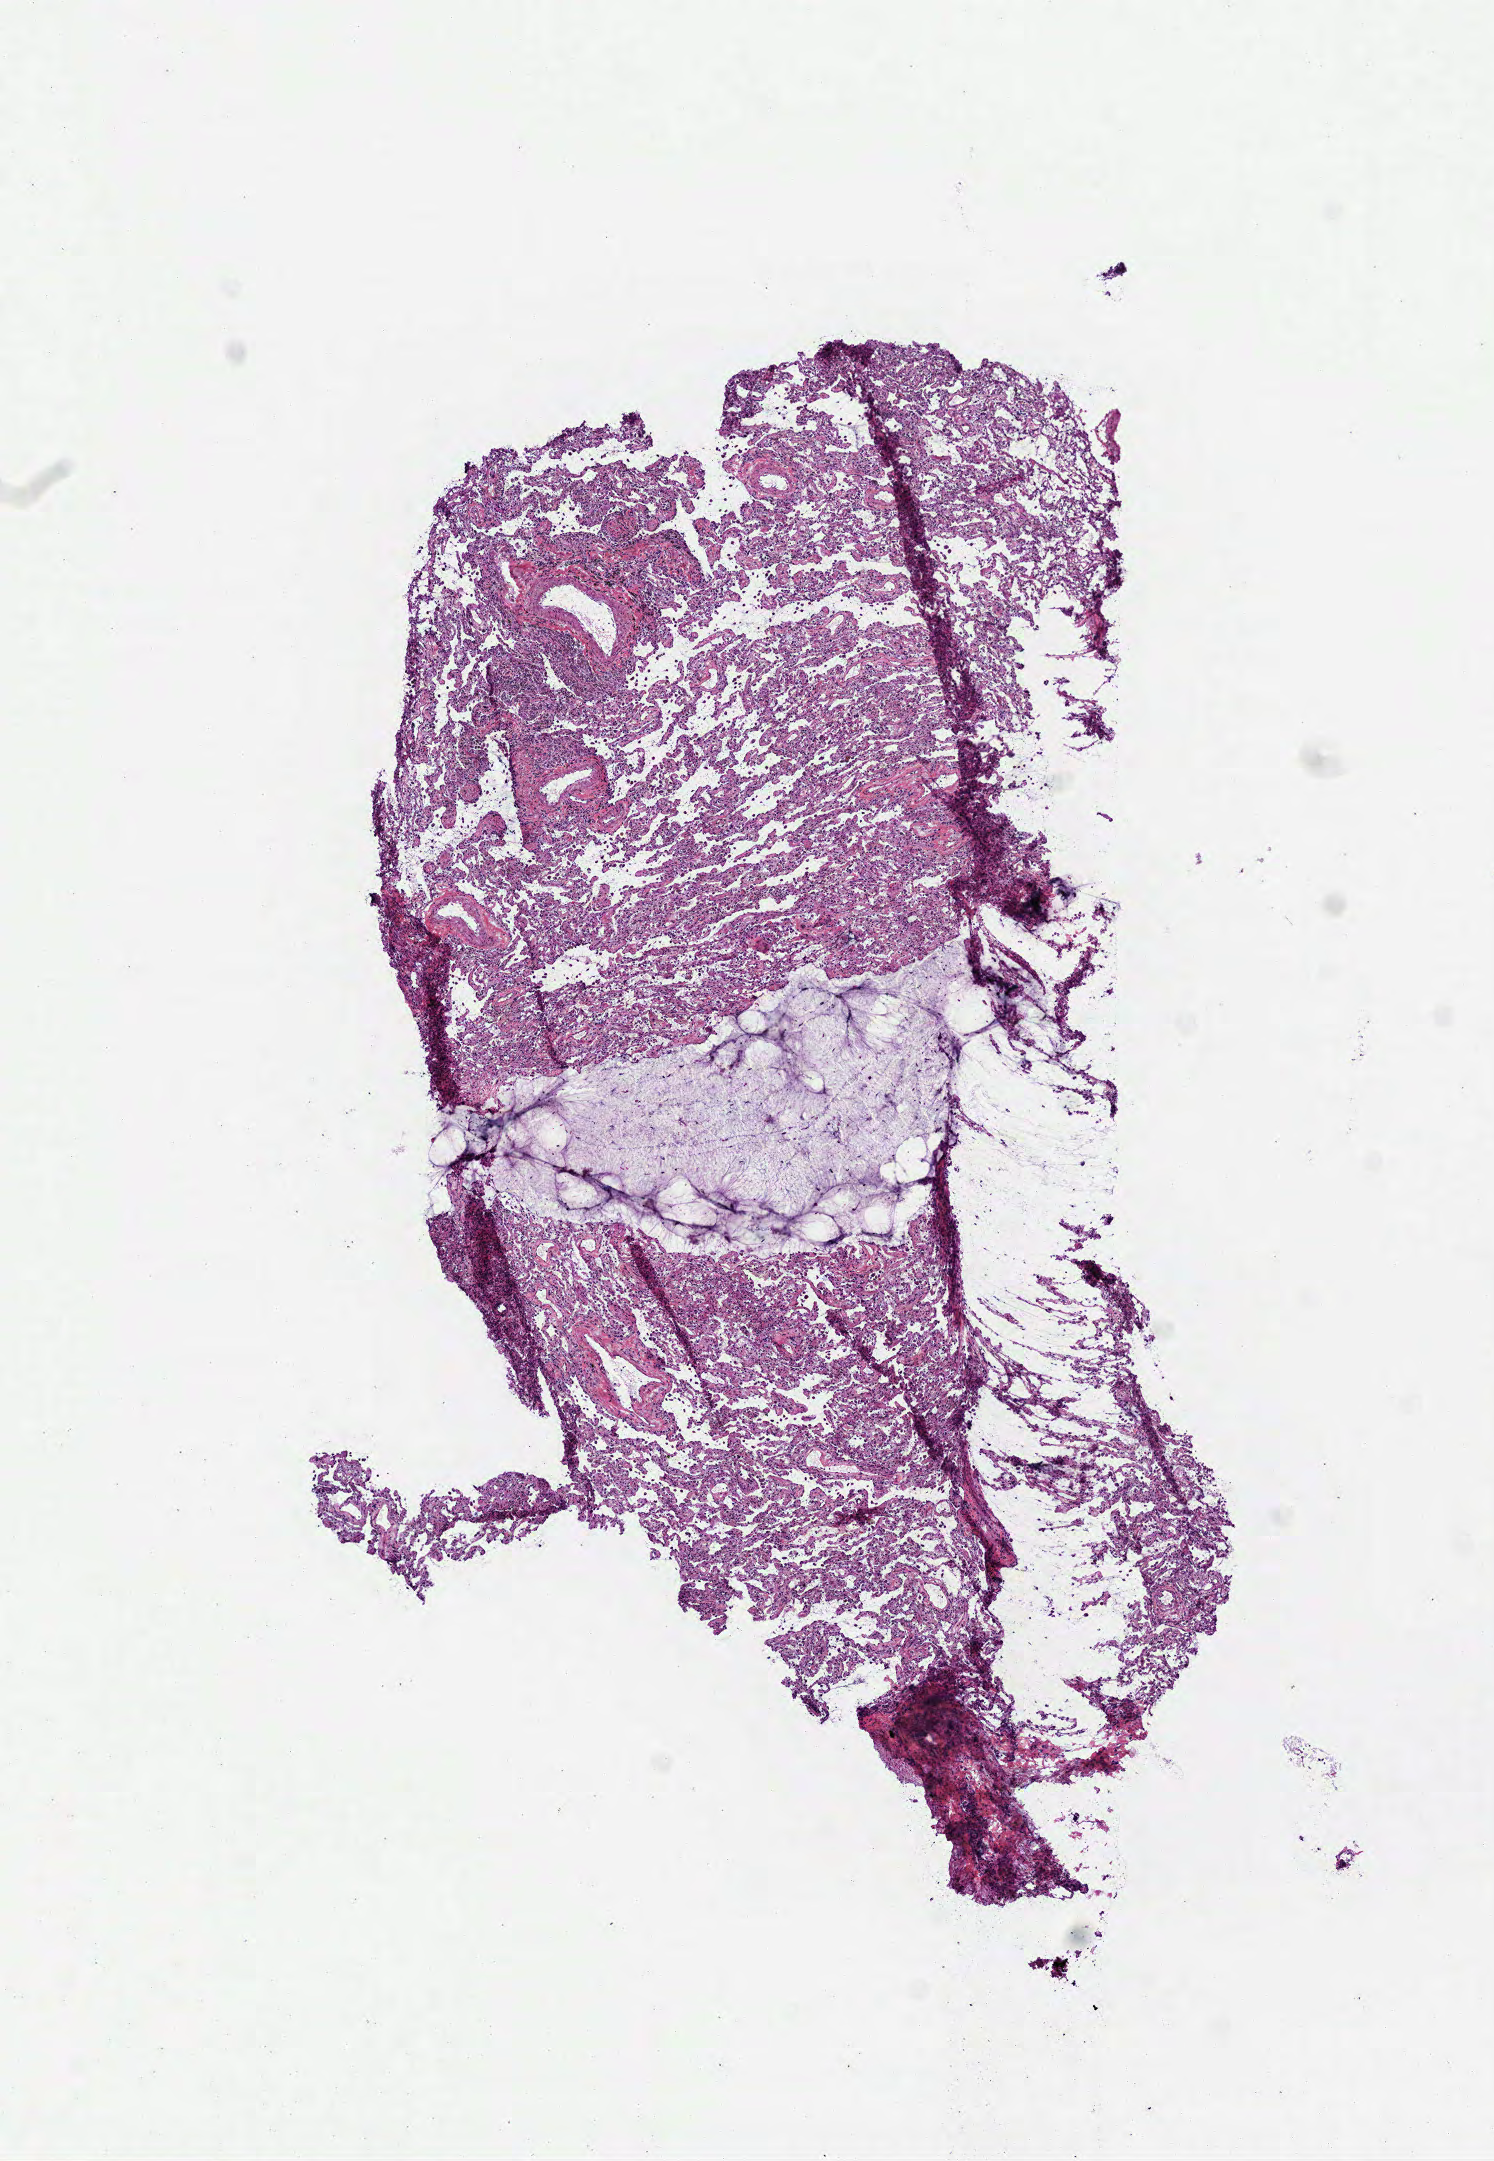
H&E whole-slide image, shown as a low-resolution overview of the whole scanned area (about 6.0 x 8.7 mm), frozen section from the top of the tissue portion, sample: solid tissue normal (non-tumour tissue), lung. Male patient; age at initial diagnosis 68 years.
- this section: solid tissue normal (non-tumour) sample from the same patient
- patient diagnosis: Squamous cell carcinoma, NOS